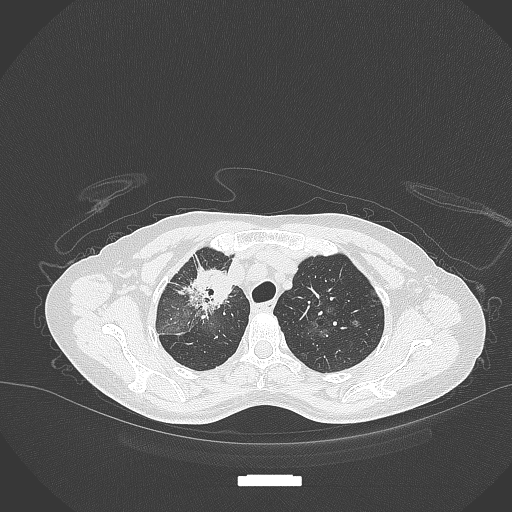
Chest CT, one axial slice. Slice 261 of 284 in the series (ordered by position). Reconstruction kernel B70f. 120 kVp. Lung window (W 1500 / L -600 HU). 1 mm slice thickness. 512 × 512 image matrix. Female patient, age 59 years. Case-level facts recorded for this patient, not image findings: clinical TNM (as recorded): T3 N0 M0; histopathological grade: G1.
Outlined on this slice (bounding box drawn by a radiologist):
- lung tumour (recorded histology: adenocarcinoma): bounding box <178,261,233,313> (left, top, right, bottom; pixels)